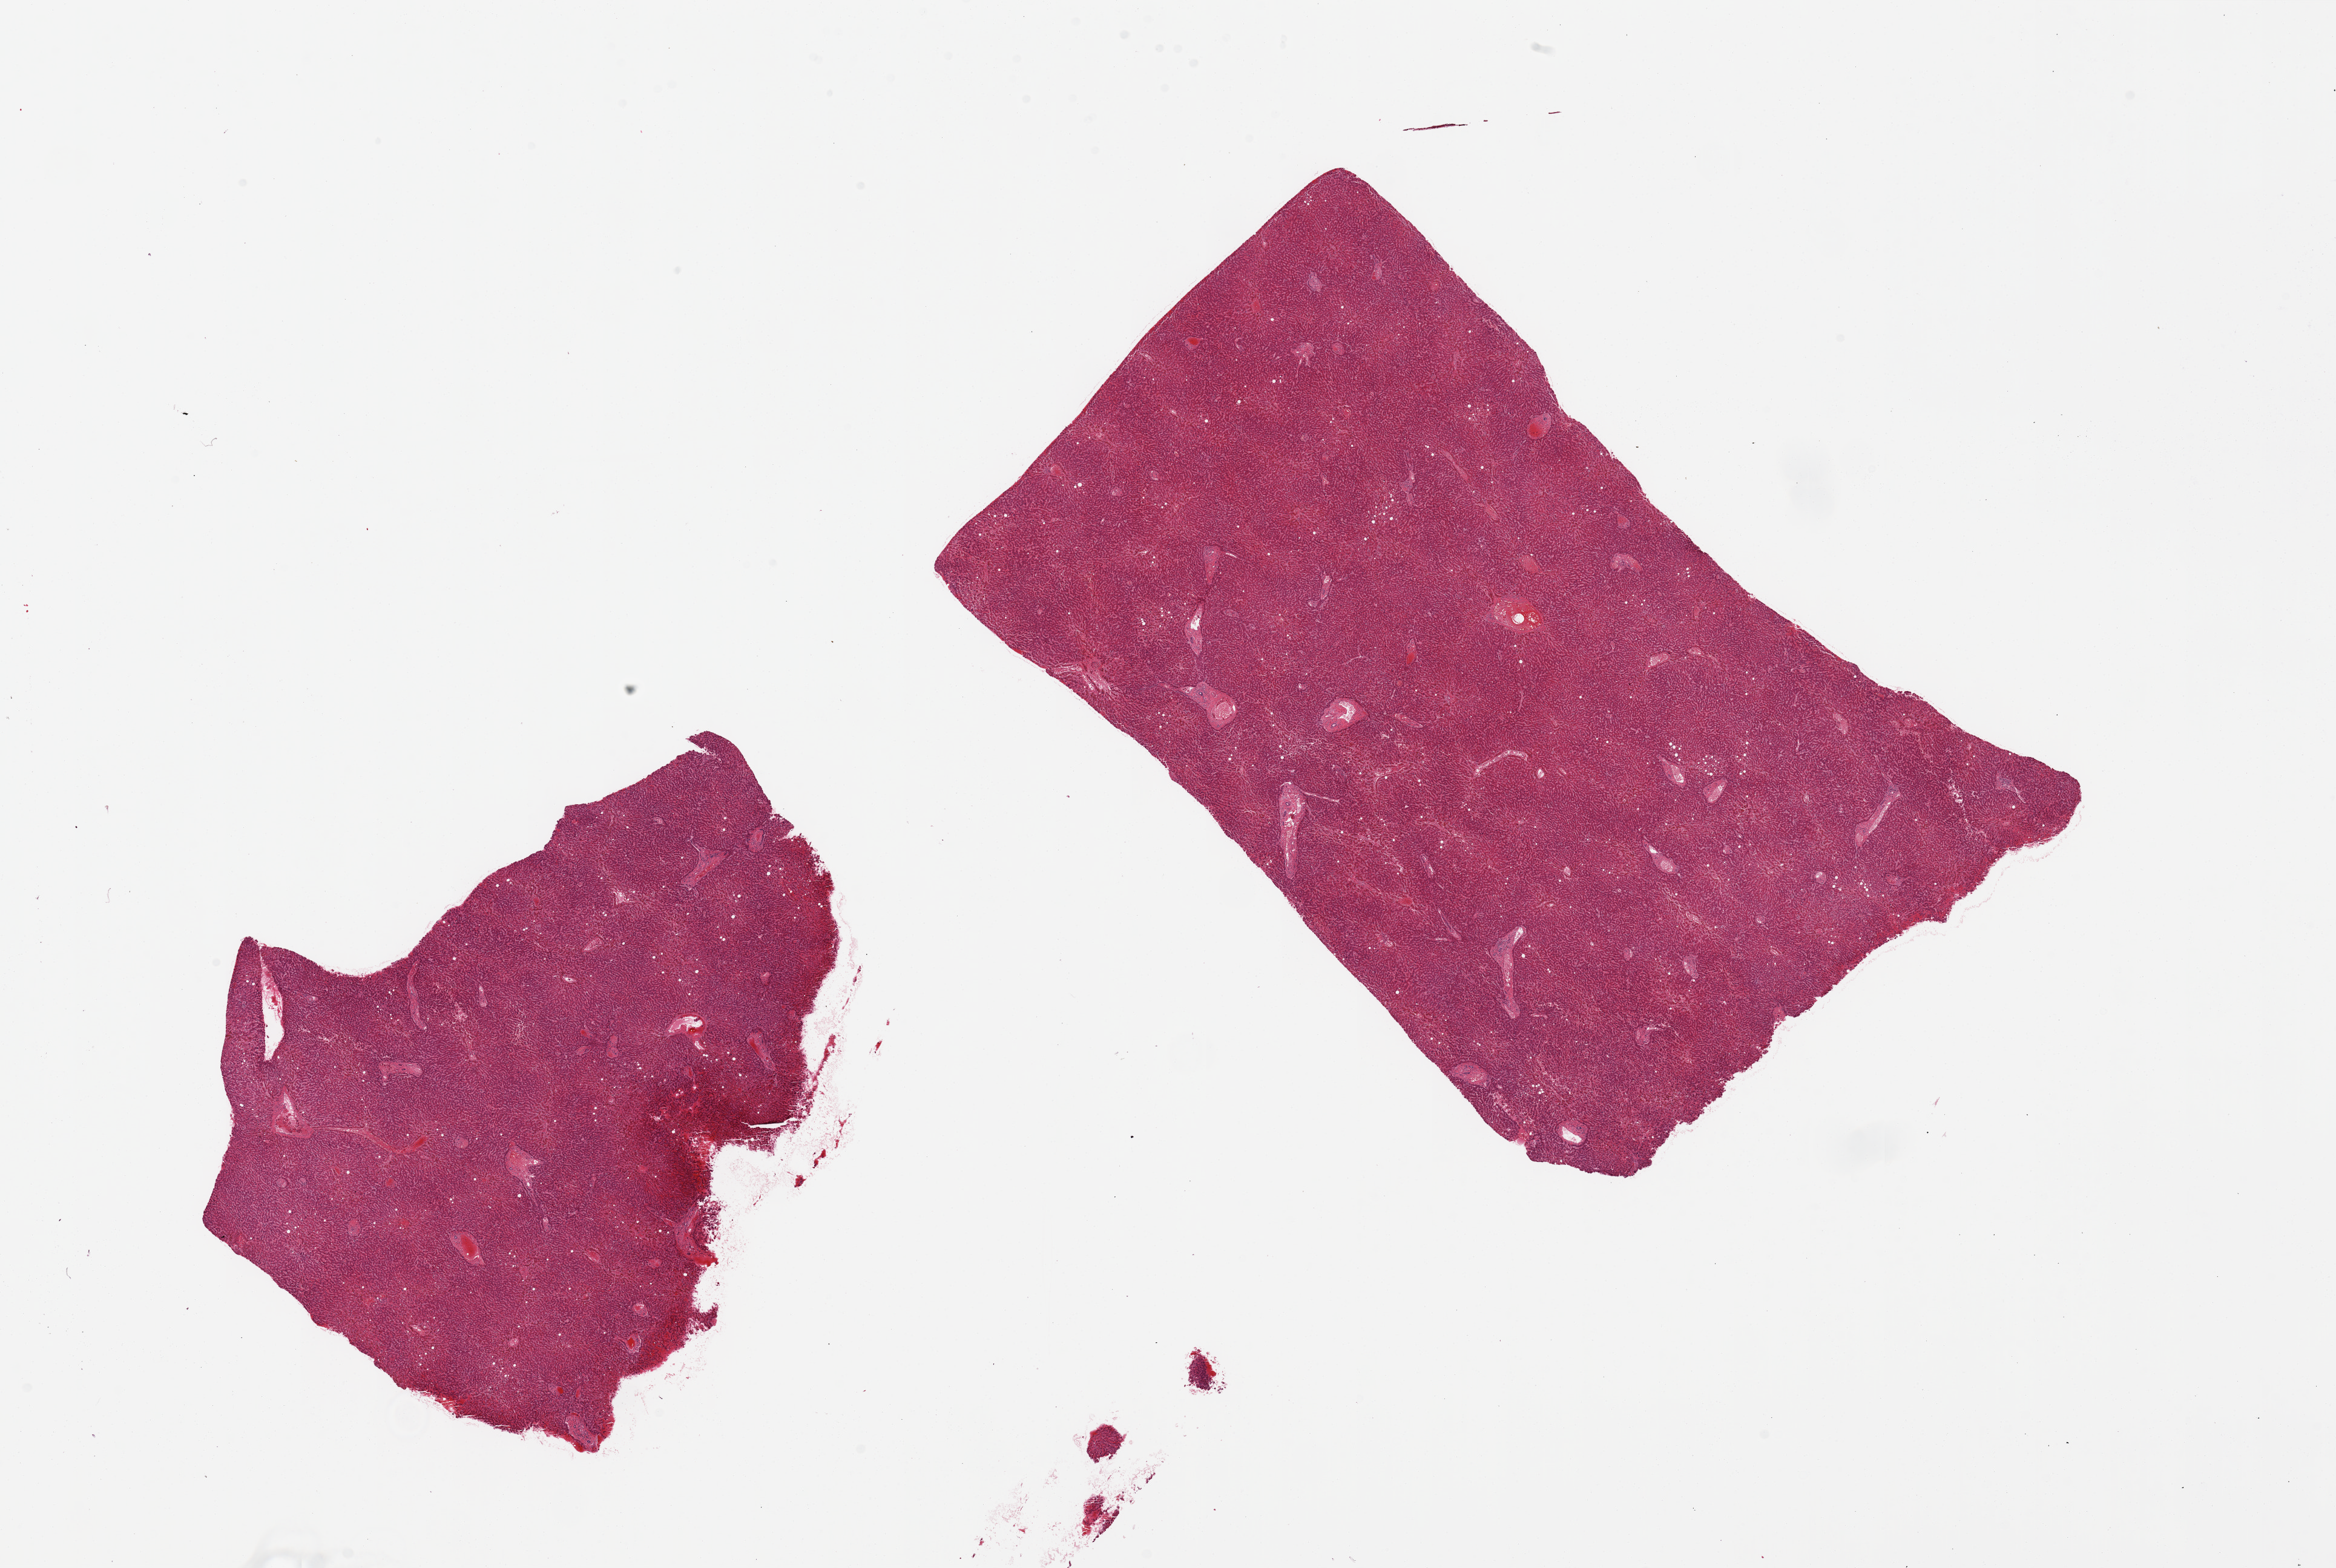
Whole-slide image, haematoxylin and eosin stain, a low-resolution overview of the entire scanned area, about 30.5 x 20.5 mm; PAXgene-fixed paraffin-embedded (PFPE) section; sampled site (target tissue): liver; tissue donor sample. Donor sex: male.
Review note (as recorded): 2 pieces; <5% macrovesicular steatosis.